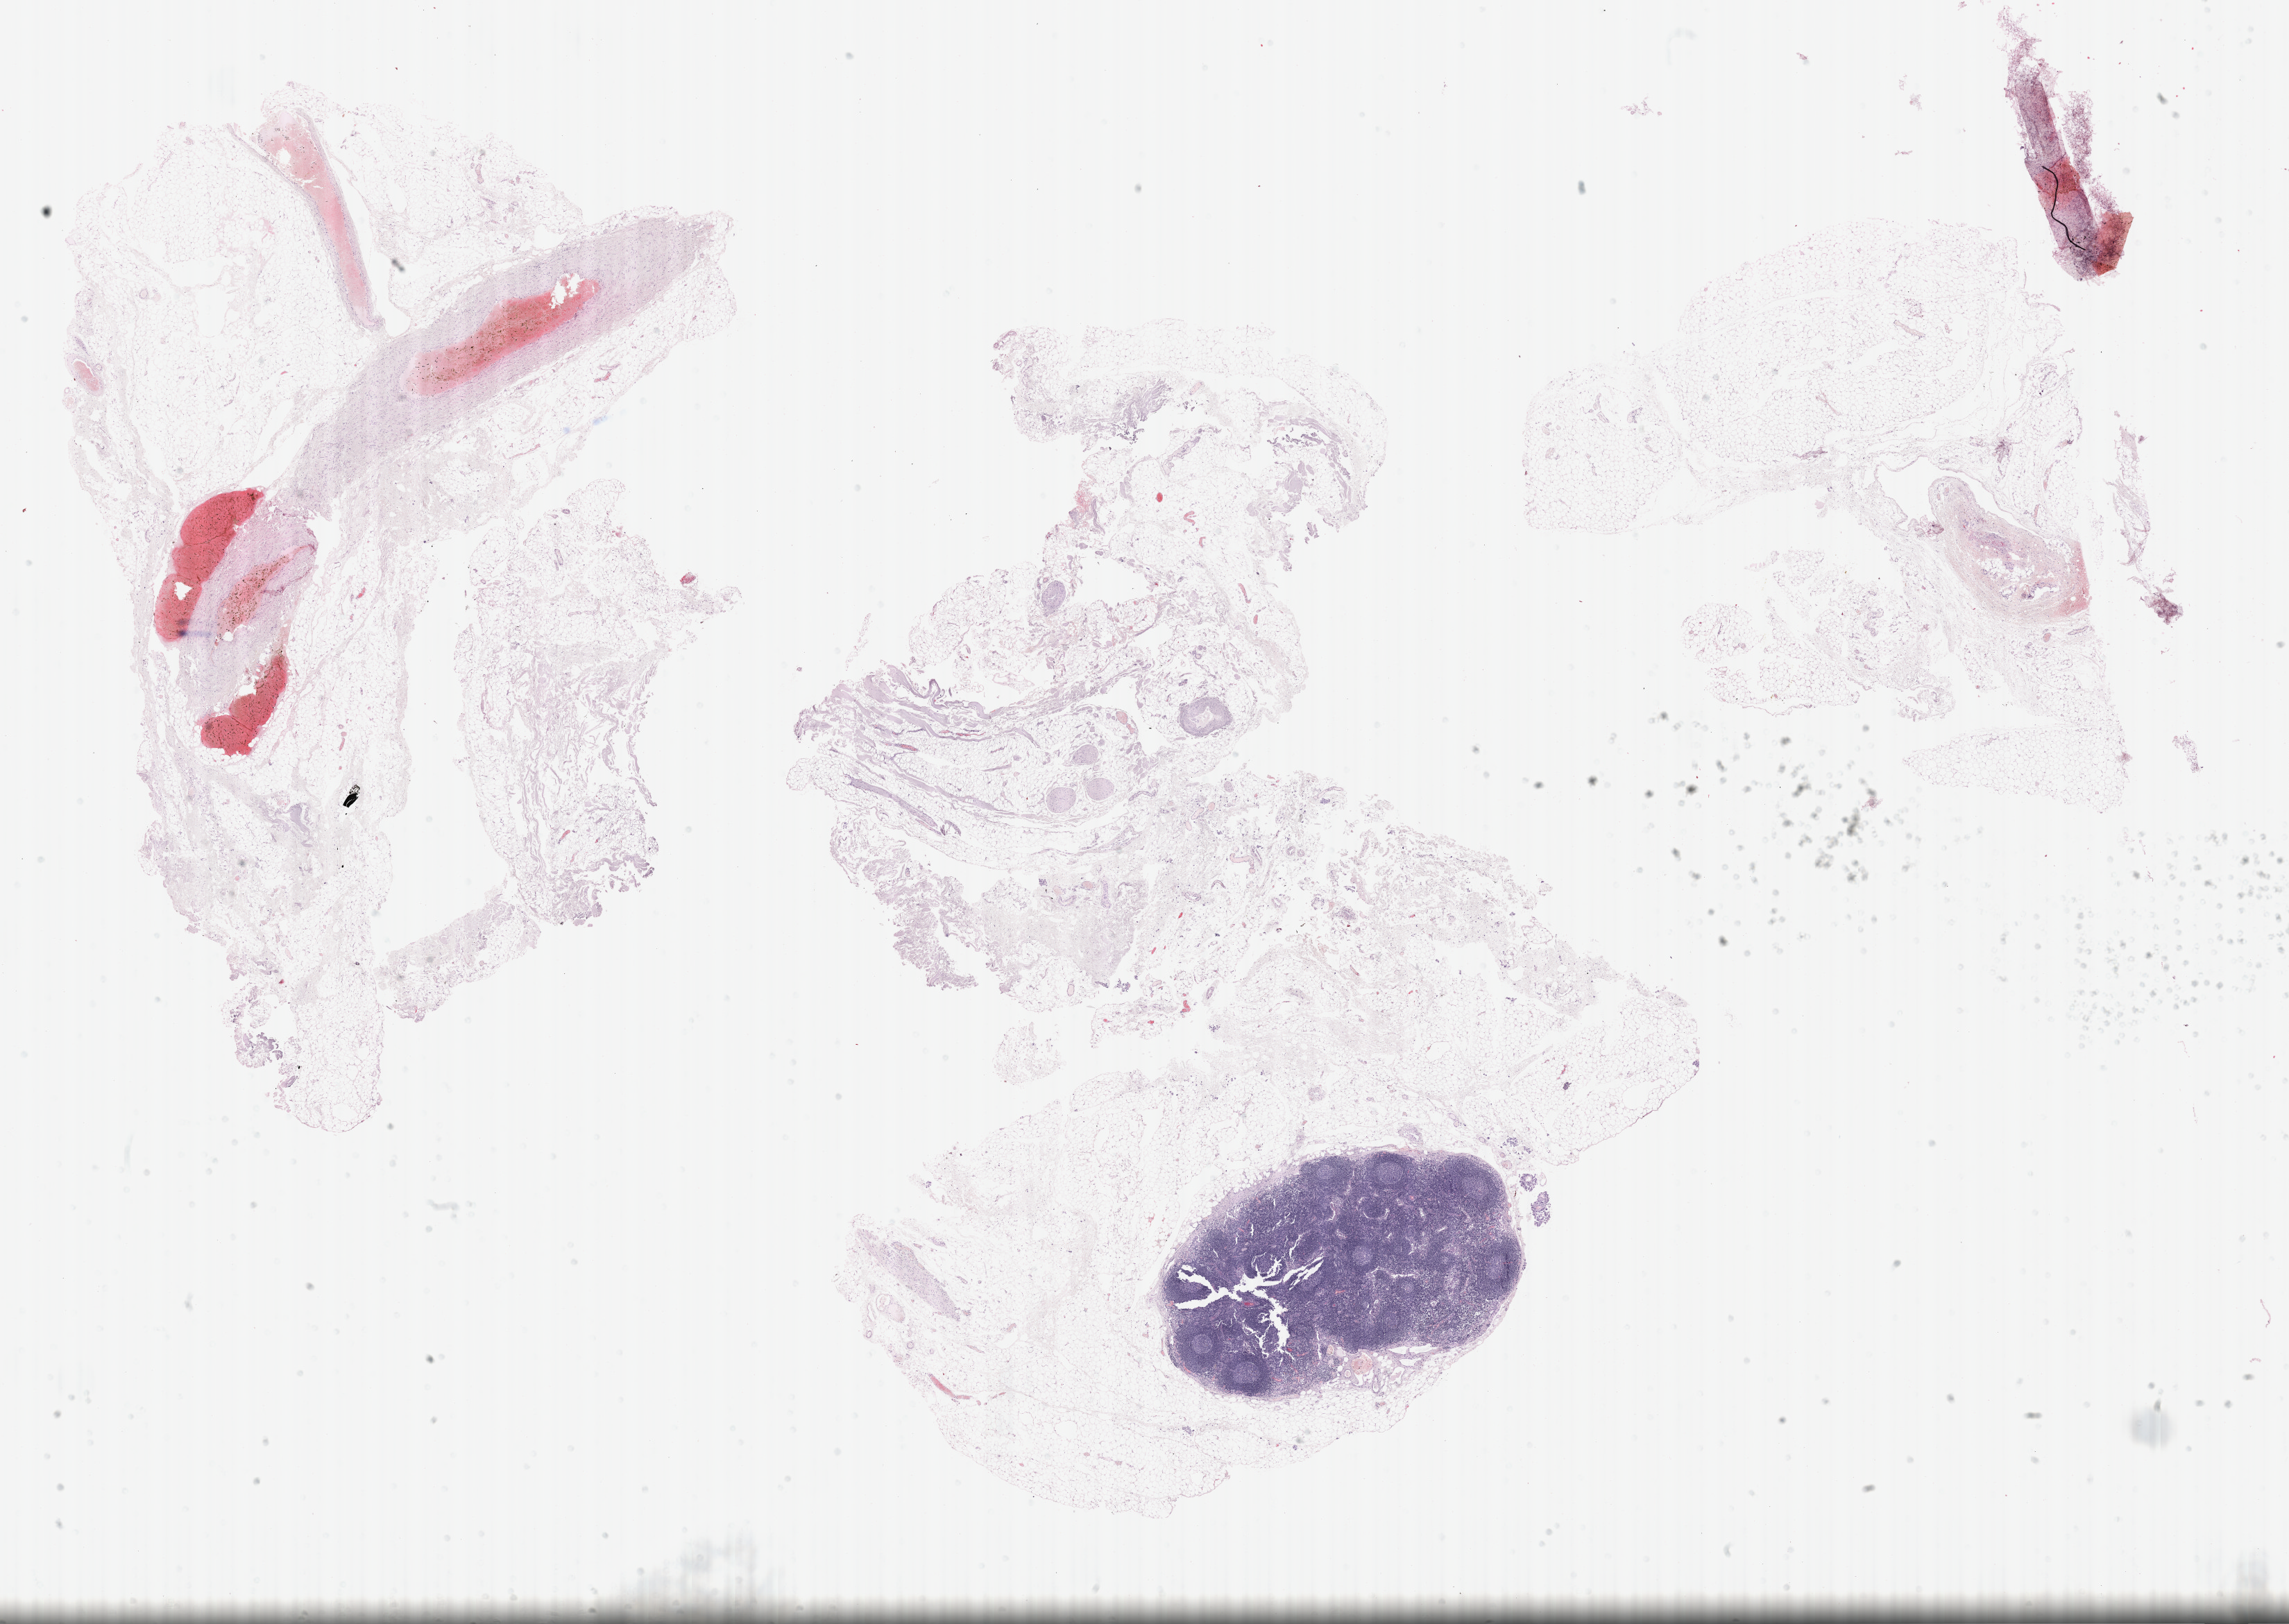
Whole-slide histology image, Hematoxylin and eosin (H&E) stained — low-resolution overview of the scanned area, about 26.7 x 18.9 mm; FFPE section; primary tumour sample from the skin. Male, age 70 years at initial diagnosis.
Histologic diagnosis: Malignant melanoma, NOS.